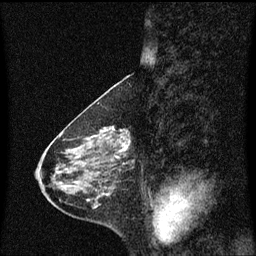
Breast MRI (dynamic contrast-enhanced), one sagittal slice; dynamic contrast-enhanced series, image 2 of 3 at this slice position (ordered by acquisition); 1.5 T; TE 4.2 ms, TR 8.4 ms; 2 mm slice thickness; 256 × 256 image matrix, field of view 200 × 200 mm. Female patient, age 58 years.
Outlined on this slice (semi-automatically segmented with operator editing):
- analysis volume of interest (the breast-tissue region the enhancement analysis was run in; not a lesion): bounding box <100,126,131,160> (left, top, right, bottom; pixels)
- tumour enhancement mask (voxels above the 70 % enhancement threshold inside the analysis volume of interest): <100,126,131,160>